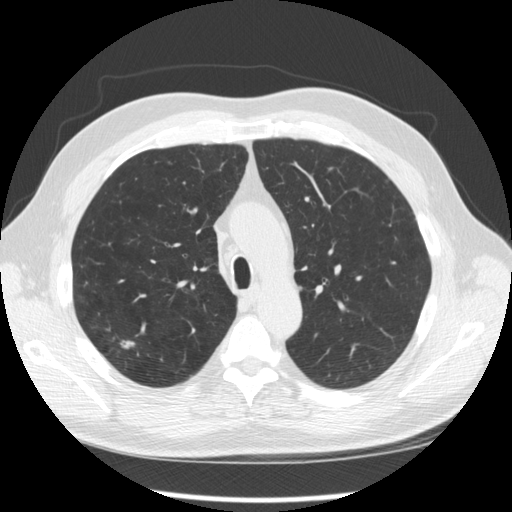
Chest CT (low-dose screening protocol), one axial image, second annual screen, lung window (W 1500 / L -600 HU), 120 kVp. Male, age 64 years at enrolment. Former smoker at enrolment.
Expert-annotated lung lesion, box from (x=103, y=327) to (x=149, y=368) px. The screening reader recorded 3 non-calcified nodules or masses ≥4 mm on this exam (right upper lobe, right upper lobe, right upper lobe); which of them this box marks is not recorded. Official screen result: positive, other. Lung cancer was diagnosed 411 days after this screen (after the third annual screen): adenocarcinoma, NOS, right upper lobe, moderately differentiated (G2), stage IA (AJCC 6th edition), 14 mm at pathology.